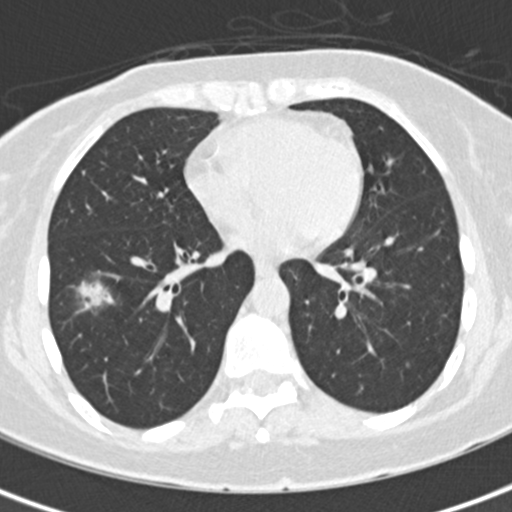
Low-dose screening chest CT, one axial slice. Position 73 of 171 along the scan axis. Reconstruction kernel B30f. Lung window (W 1500 / L -600 HU). 512 × 512 image matrix, field of view 284 × 284 mm.
Annotated regions visible in this slice (outlined manually by an expert reader):
- lesion 1 (tumor, lower lobe of right lung): box from (x=76, y=280) to (x=114, y=313) px